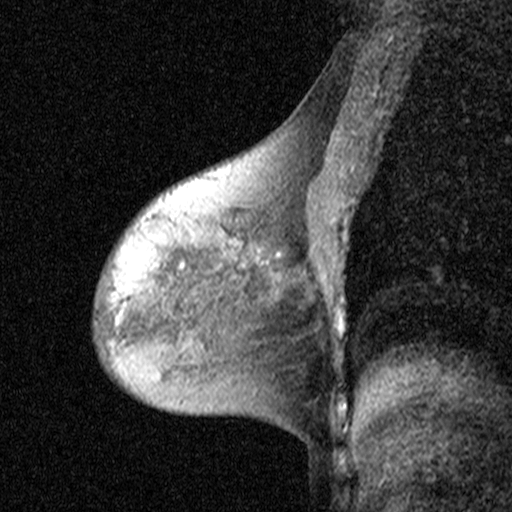
Breast MRI (dynamic contrast-enhanced), one sagittal slice; position 26 of 44 along the scan axis; dynamic contrast-enhanced study with each time point stored as its own series, time point 2 of 3 at this slice position (early post-contrast, ordered by acquisition time); 1.5 T; TE 4.5 ms, TR 11 ms; 3 mm slice thickness; 512 × 512 image matrix. Patient: female, 53 years. Case-level facts recorded for this patient, not image findings: setting: breast cancer imaged before/during neoadjuvant chemotherapy; receptor status: HR-positive, HER2-negative.
Outlined on this slice (semi-automatically segmented with operator editing):
- analysis volume of interest (the breast-tissue region the enhancement analysis was run in; not a lesion): box from (x=186, y=216) to (x=307, y=311) px
- tumour enhancement mask (voxels above the 90 % enhancement threshold inside the analysis volume of interest): (x=231, y=240)–(x=281, y=257)